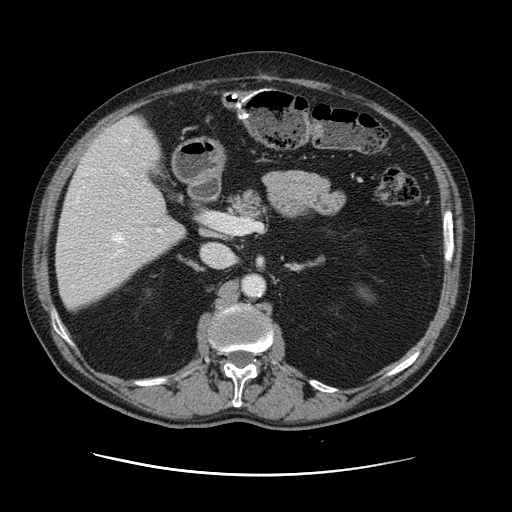
Contrast-enhanced abdominal CT, one axial slice; position 66 of 141 along the scan axis; 120 kVp; intravenous contrast given; soft-tissue window (W 400 / L 40 HU); 2.5 mm slice thickness; 512 × 512 image matrix, field of view 395 × 395 mm. Male patient, age 72 years. From the clinical record (not read from this slice): diagnosis: colorectal cancer liver metastases, imaged before liver resection; multiple liver metastases: yes; largest metastasis: 5.4 cm.
Outlined on this slice (outlined manually by an expert reader):
- hepatic veins: bounding box <112,139,145,255> (left, top, right, bottom; pixels)
- liver: <57,117,184,310>
- planned liver remnant (the part of the liver to remain after resection): <56,187,184,309>
- portal vein (with intrahepatic branches): <111,227,153,239>